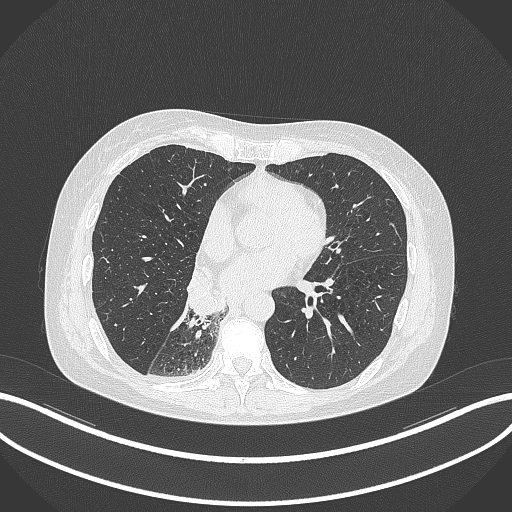
Chest CT, one axial slice. Reconstruction kernel B70f. Lung window (W 1500 / L -600 HU). 1 mm slice thickness. 512 × 512 image matrix, field of view 400 × 400 mm. Patient: female, 63 years. From the clinical record (not read from this slice): clinical TNM (as recorded): T1c N0 M0.
Structures marked on this image (rectangle marked by the reading radiologist):
- lung tumour (recorded histology: adenocarcinoma): bounding box <186,271,224,321> (left, top, right, bottom; pixels)